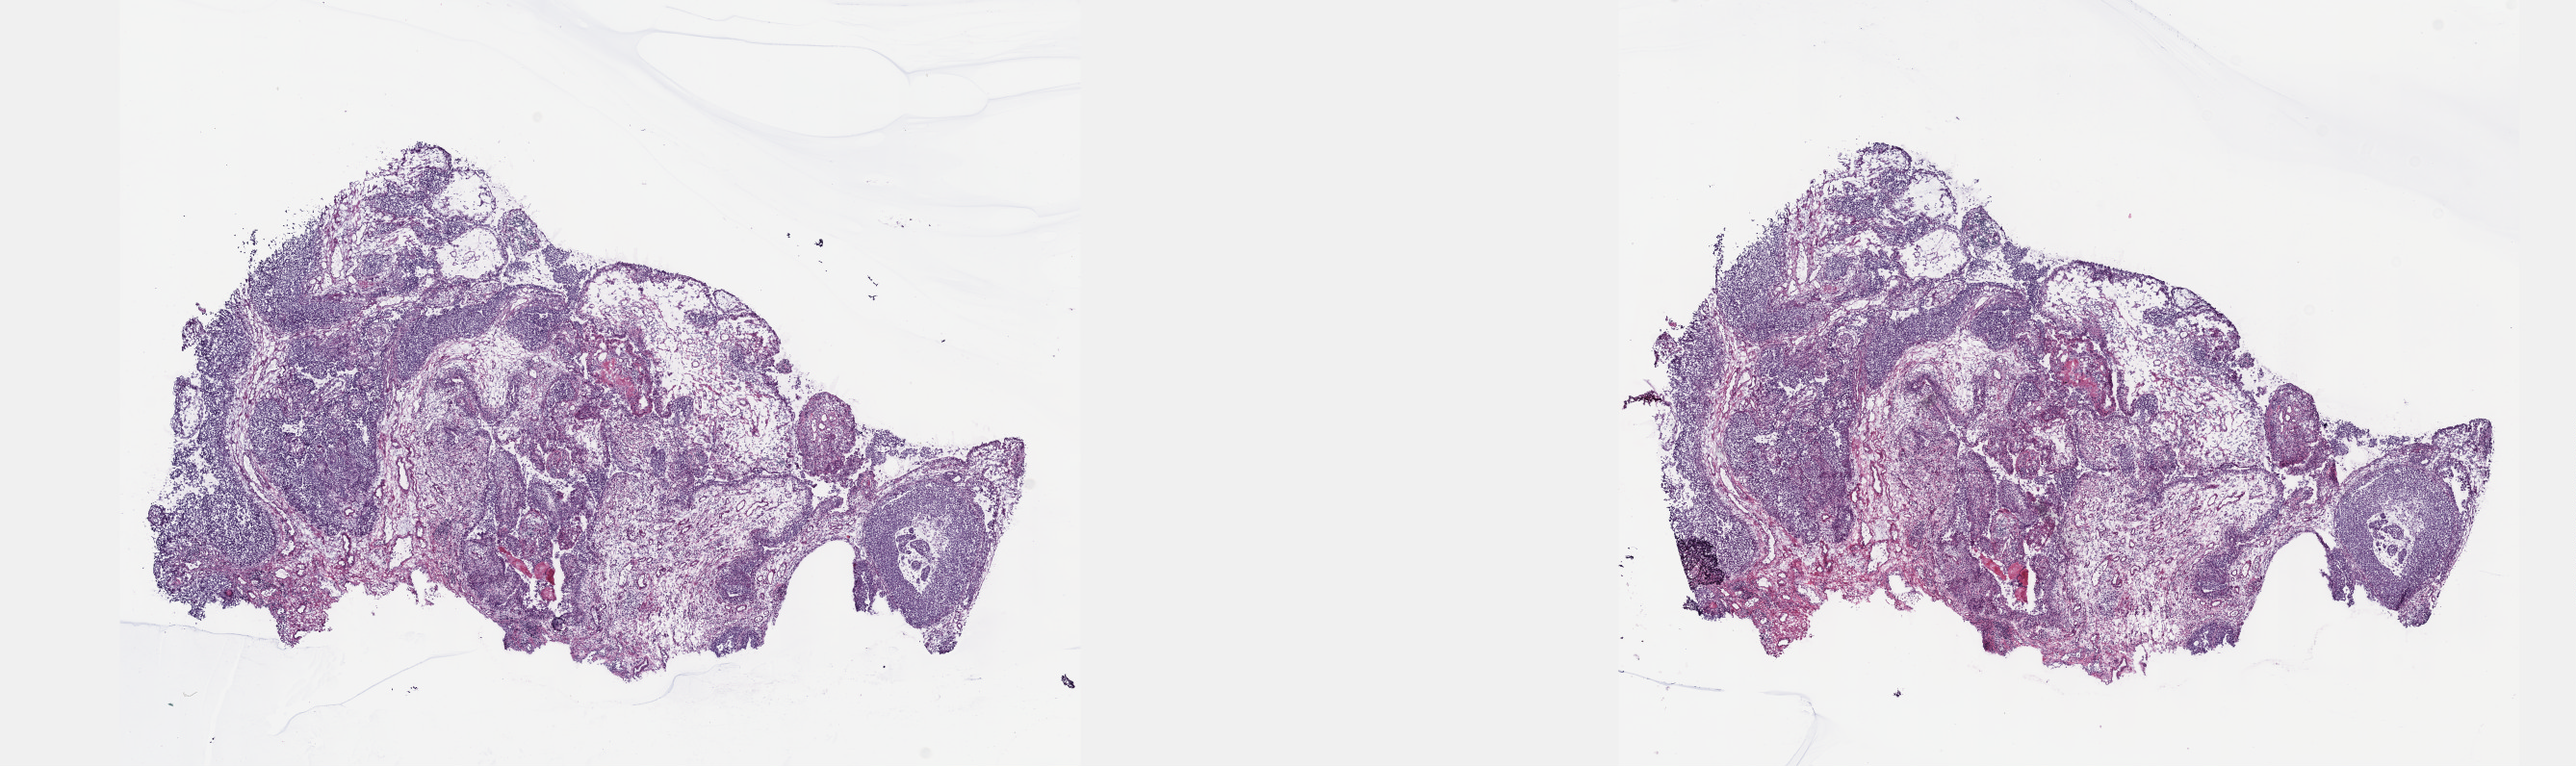
Whole-slide histology image, Hematoxylin and eosin (H&E) stained, shown as a low-resolution overview of the whole scanned area (about 21.6 x 6.4 mm). Frozen section from the top of the tissue portion. Primary tumour sample from the bladder. Male, age 71 years at initial diagnosis. Histologic grade: high grade. Slide review estimates, as recorded: tumour cells 65%, tumour nuclei 65%, normal cells 3%, stromal cells 32%, necrosis 0%. Infiltration values recorded for this section: lymphocyte infiltration 4%, monocyte infiltration 2%, neutrophil infiltration 4%.
* pathologic diagnosis: Papillary transitional cell carcinoma
* lymph nodes positive (case pathology): 0 of 16 examined
* AJCC pathologic stage: II